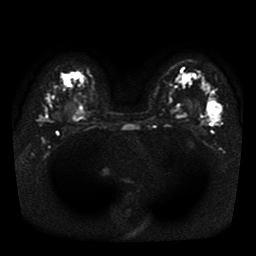
Breast MRI, one axial slice; slice 29 of 41 in the series (ordered by position); diffusion-weighted series; image 2 of 4 stored at this slice position (different b-values; order by instance number); 1.5 T; 5 mm slice thickness; 256 × 256 image matrix, field of view 330 × 330 mm. Female patient.
Annotated regions visible in this slice (expert manual segmentation):
- tumour on diffusion-weighted imaging: bounding box <212,105,221,123> (left, top, right, bottom; pixels)